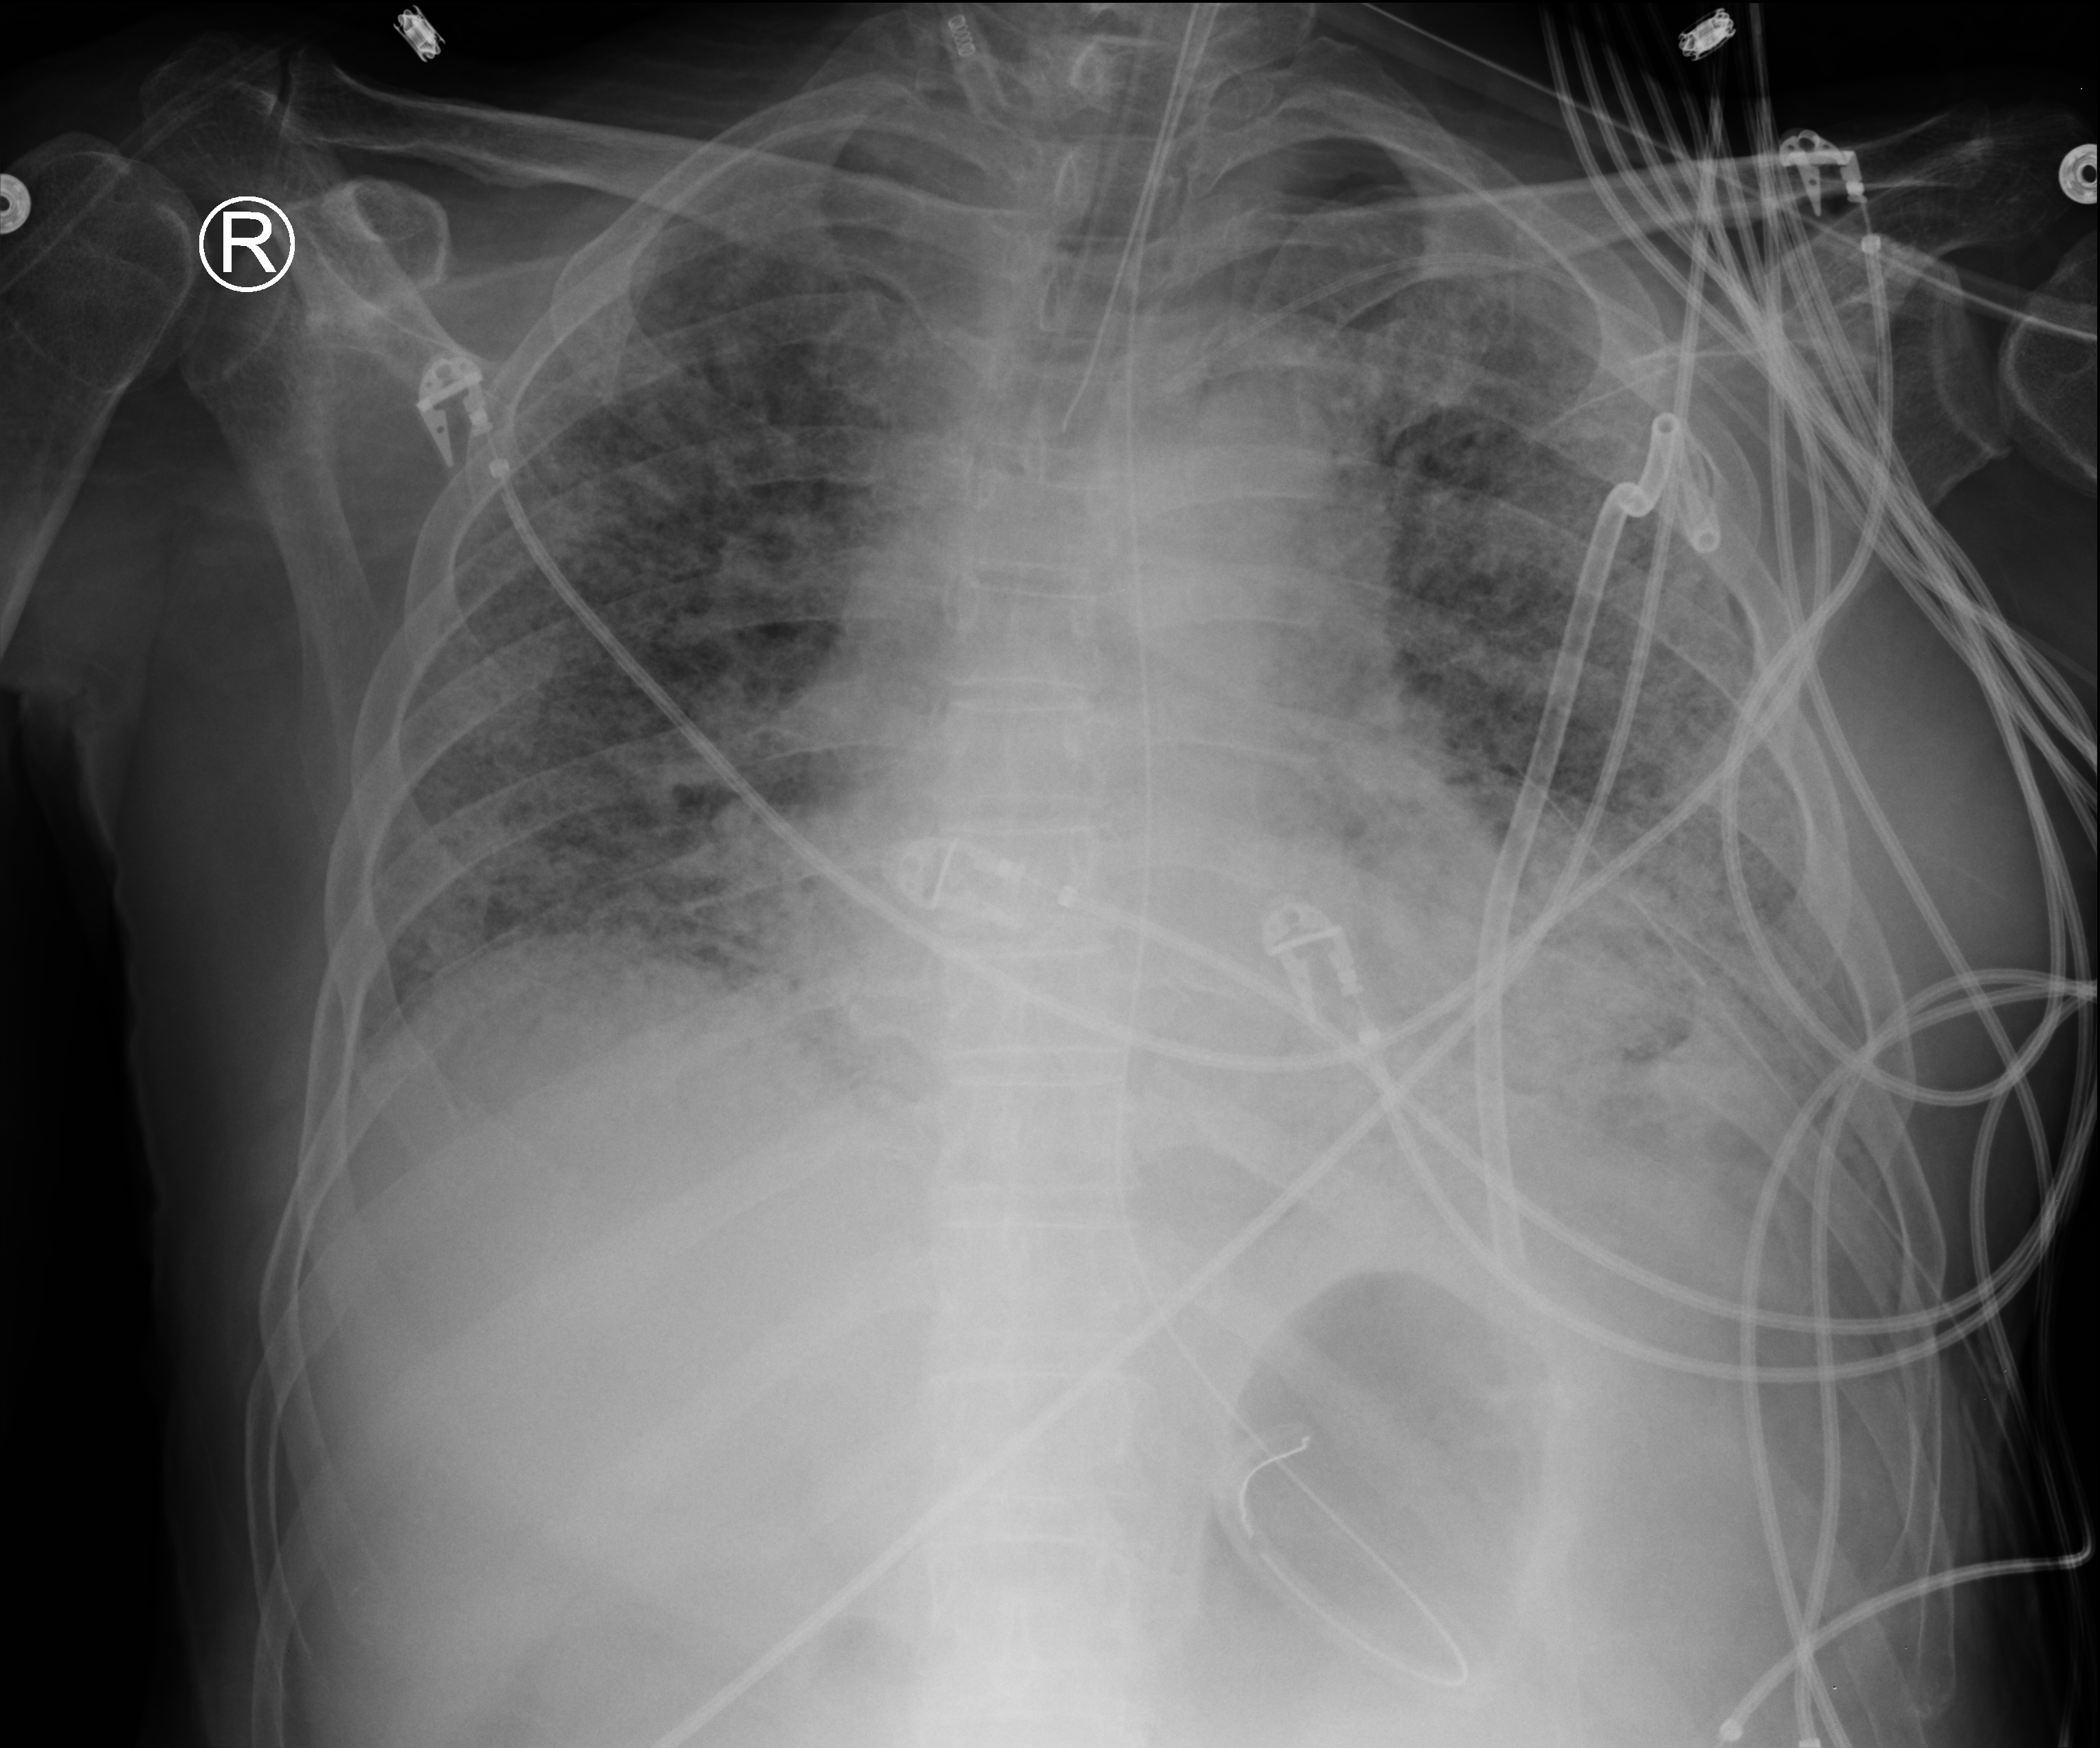
Bedside chest radiograph (computed radiography), anteroposterior (AP) projection. Patient hospitalised with COVID-19; male, aged 60–74 years.
Admission-level facts for this patient (not findings on this image; timing relative to this image not recorded): mechanically ventilated during this hospital stay: yes; admitted to intensive care during this hospital stay: yes.